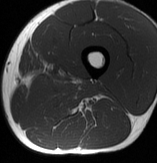
MRI of an extremity soft-tissue mass, one axial slice. MR volume resampled by the dataset authors to the PET/CT grid (not the native acquisition matrix). 157 × 163 image matrix. Male patient. From the clinical record (not read from this slice): histological type: extraskeletal osteosarcoma; grade: high; site of the primary tumour: left adductur.
Annotated regions visible in this slice (expert contour drawn on MRI and transferred to this co-registered scan by the dataset authors):
- gross tumour volume (mass): bounding box (x1, y1, x2, y2) in pixels: (26, 76, 100, 104)